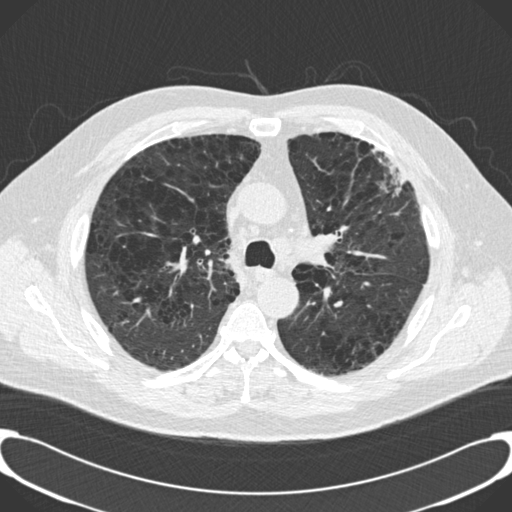
Chest CT (low-dose screening protocol), one axial image, third screening round (two years after baseline), lung window (W 1500 / L -600 HU), 120 kVp, slice 53 of 189 in the series, 512 × 512 image matrix, field of view 380 × 380 mm. Male, age 59 years at enrolment.
- Expert-annotated lung lesion, bounding box [x1, y1, x2, y2] px = [356, 143, 422, 220].
- Screening reader's record for this exam: no non-calcified nodule ≥4 mm recorded.
- Later outcome: lung cancer diagnosed 134 days after this screen — bronchiolo-alveolar carcinoma, mixed mucinous and non-mucinous, left upper lobe, stage IA (AJCC 6th edition), 20 mm at pathology.